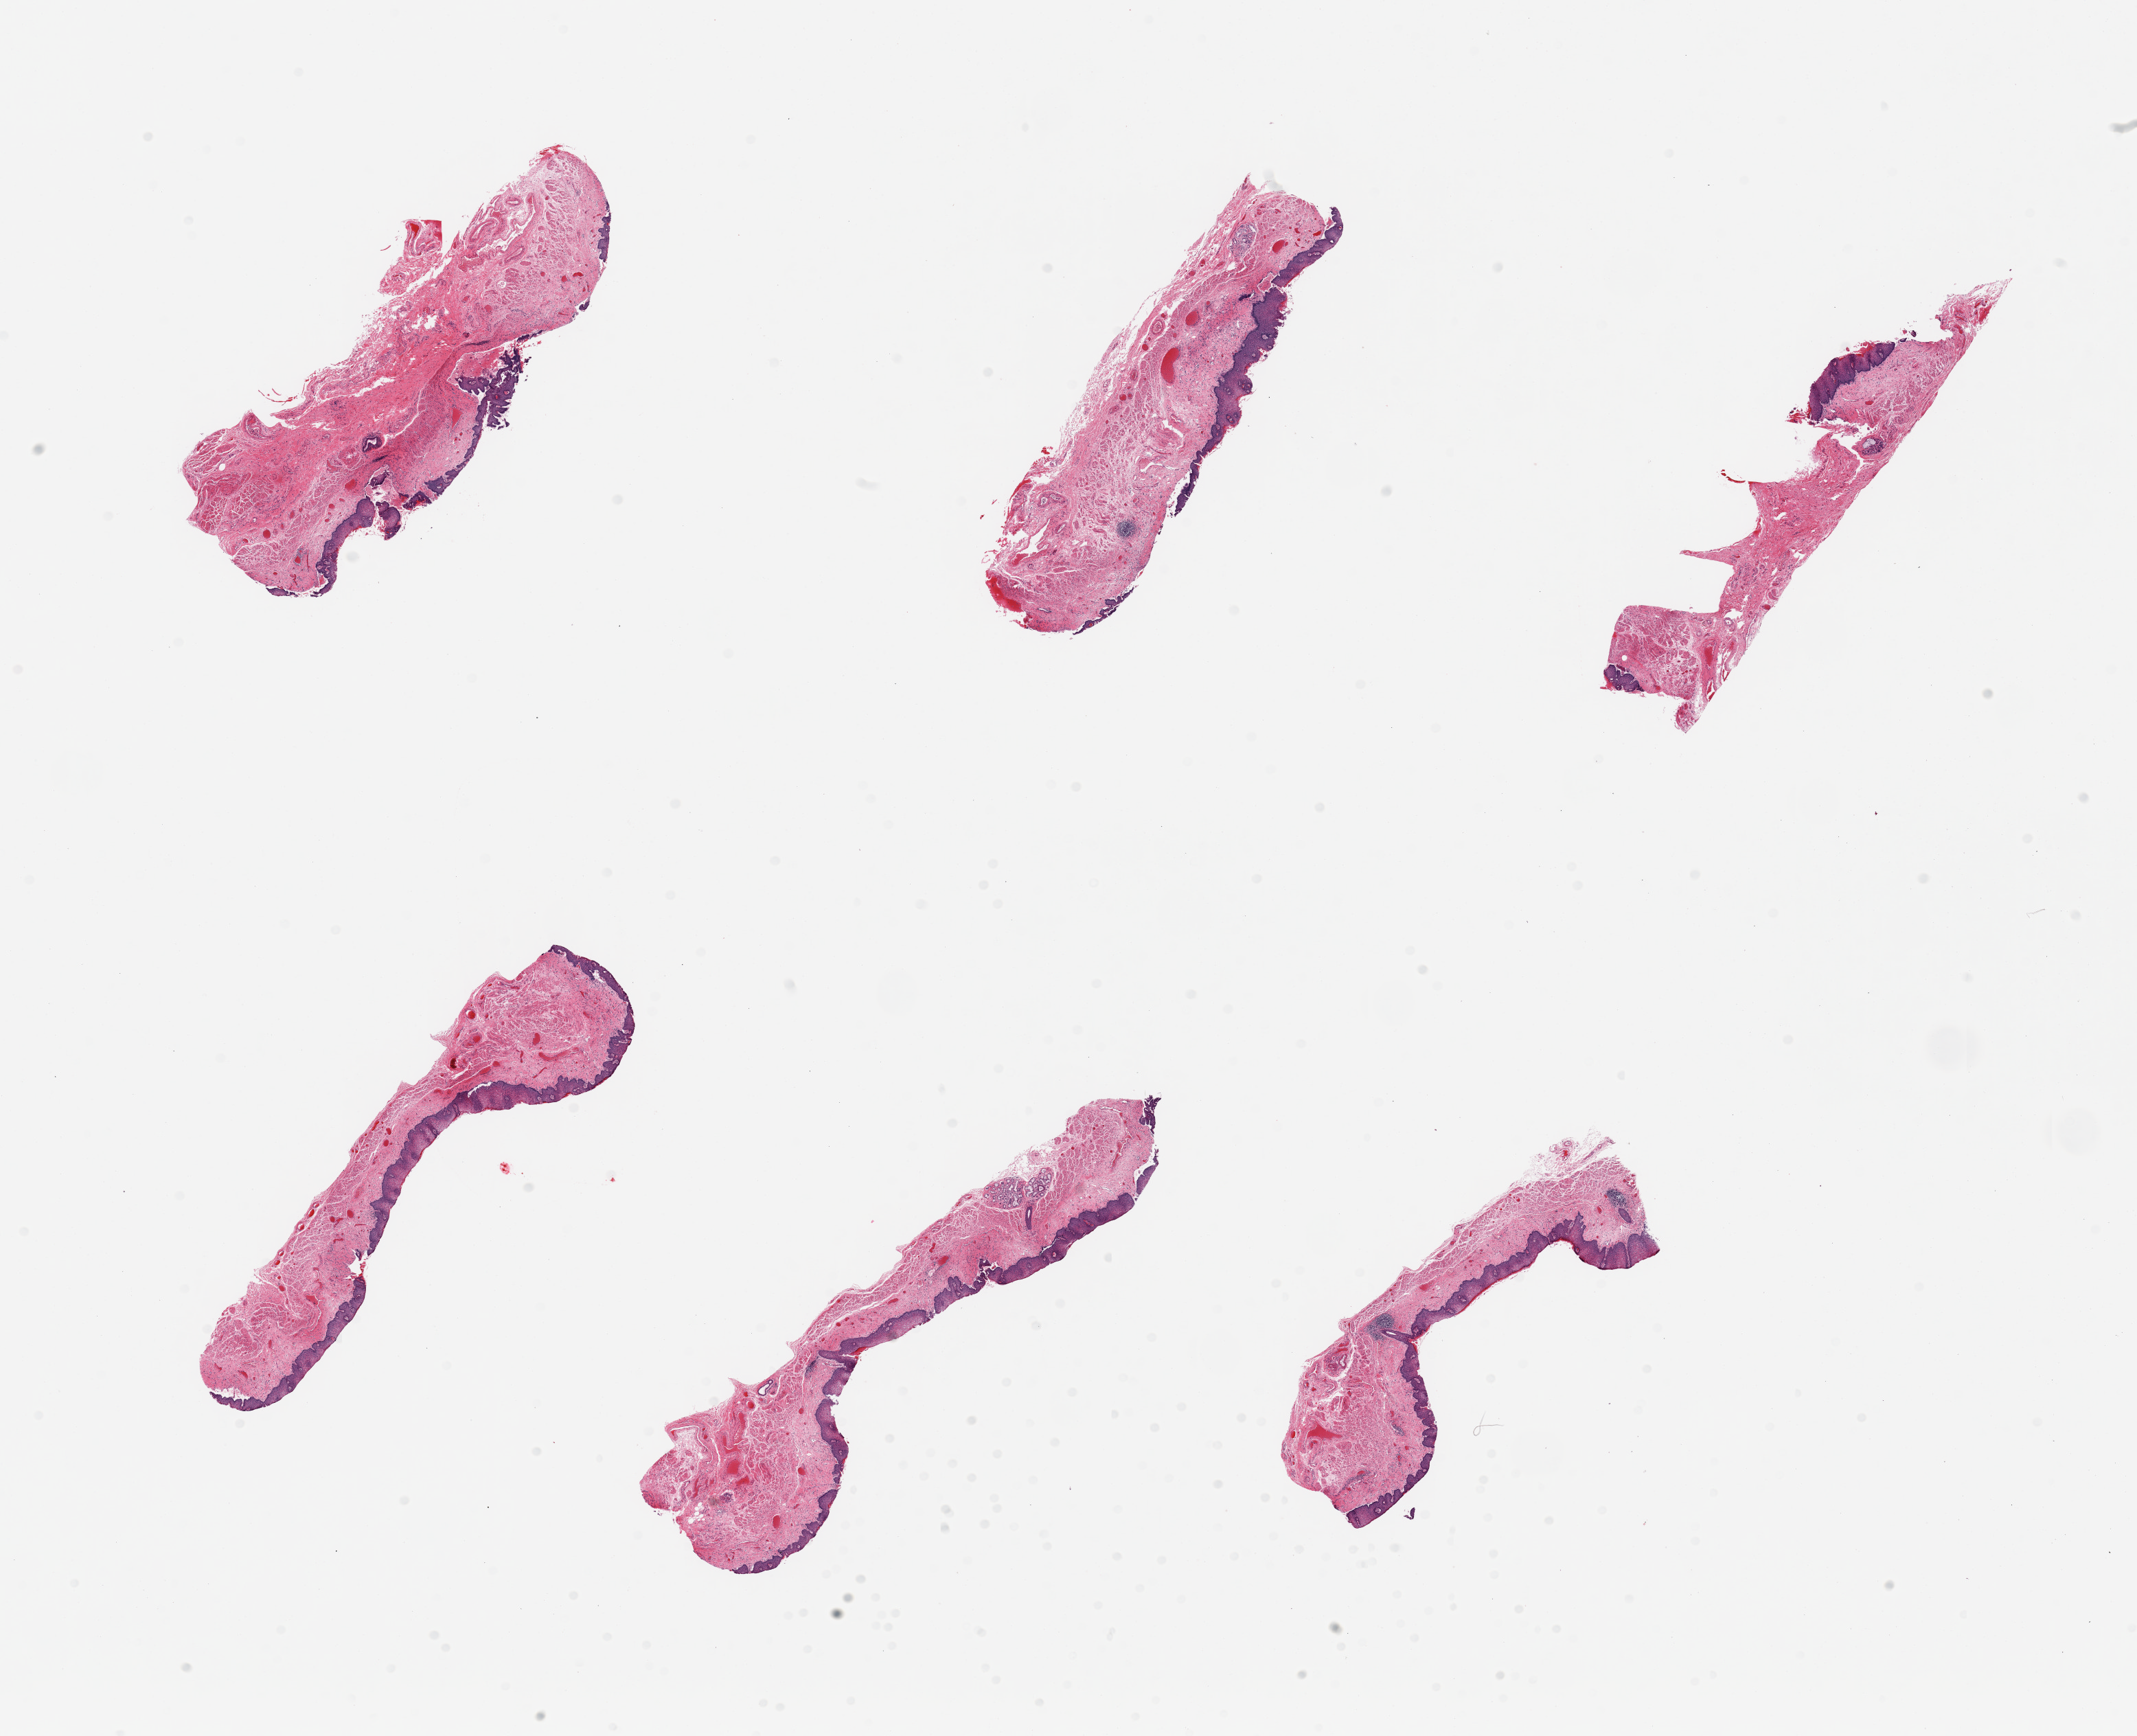
Digitized hematoxylin and eosin (H&E)-stained section, whole scanned area (about 24.6 x 20.0 mm, slide scanned at 20x) shown as a low-resolution overview, PAXgene-fixed paraffin-embedded (PFPE) section, target tissue: esophageal mucous membrane, donor tissue sample. Donor sex: male.
Pathologist's review note for this sample: 6 pieces; epithelium discontinuous in some pieces.